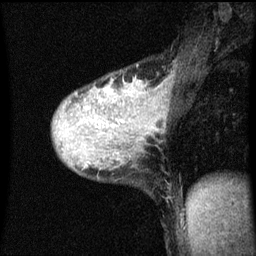
Breast MRI (dynamic contrast-enhanced), one sagittal slice. Slice 33 of 60 in the series (ordered by position). Dynamic contrast-enhanced series, image 2 of 3 at this slice position (ordered by acquisition). 1.5 T. TE 4.2 ms, TR 8.4 ms. 2 mm slice thickness. 256 × 256 image matrix. Patient: female, 36 years.
Structures marked on this image (semi-automatic segmentation, software-assisted and operator-edited):
- analysis volume of interest (the breast-tissue region the enhancement analysis was run in; not a lesion): bounding box [x1, y1, x2, y2] px = [54, 76, 163, 151]
- tumour enhancement mask (voxels above the 70 % enhancement threshold inside the analysis volume of interest): [108, 92, 111, 95]